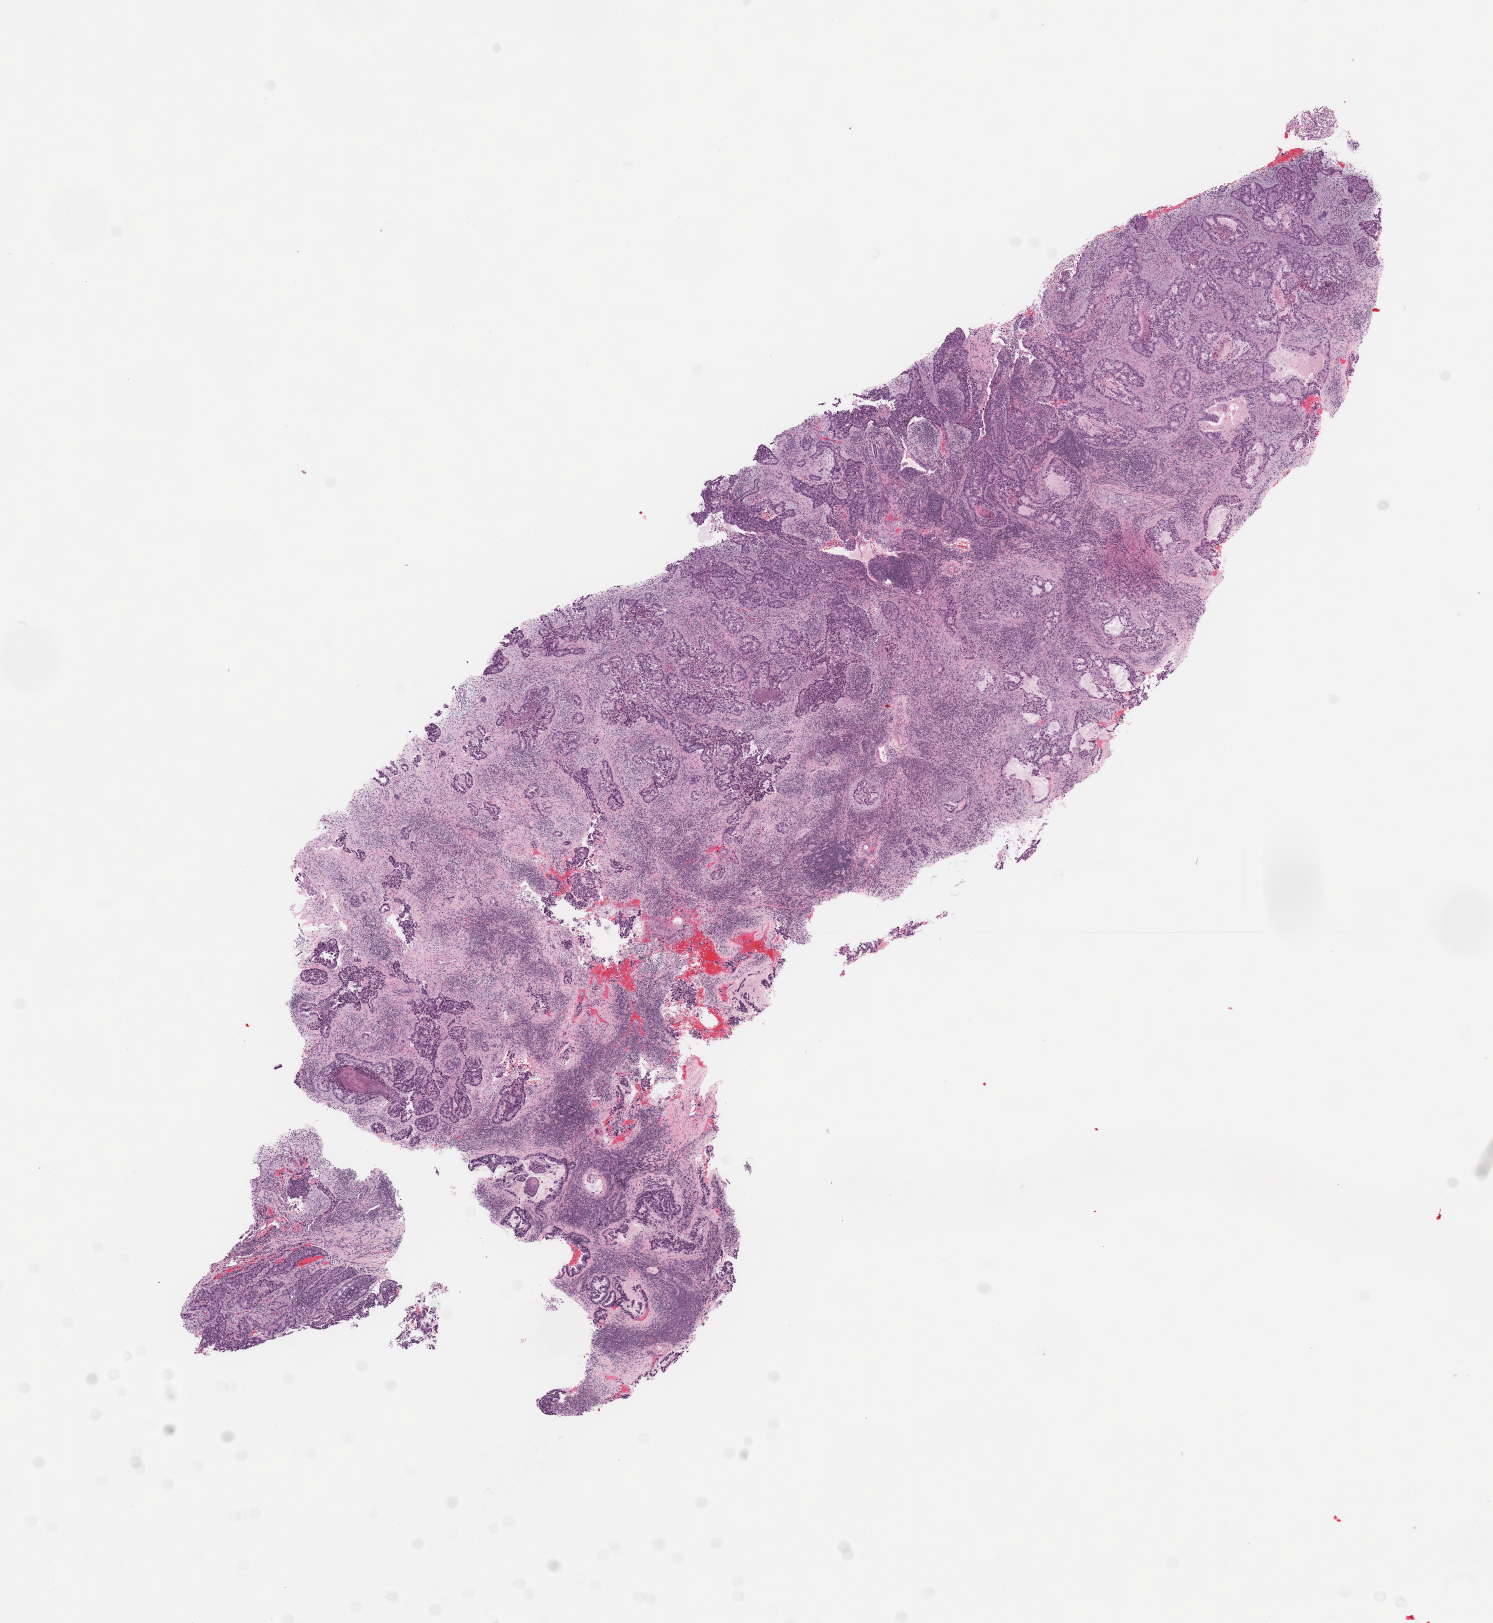
Digitized H&E-stained tissue section (whole slide) — whole scanned area (about 11.8 x 12.8 mm, from a 20x scan) shown as a low-resolution overview; tumour tissue sample, sampled site: lung. Patient: male, age 69 years. Histologic grade: G3 (poorly differentiated). Composition of this section per pathologist review: tumour nuclei 60%, necrosis 5%.
Diagnosis: Adenocarcinoma, NOS. AJCC pathologic stage: IA. Primary tumour site (as recorded): right middle lobe.